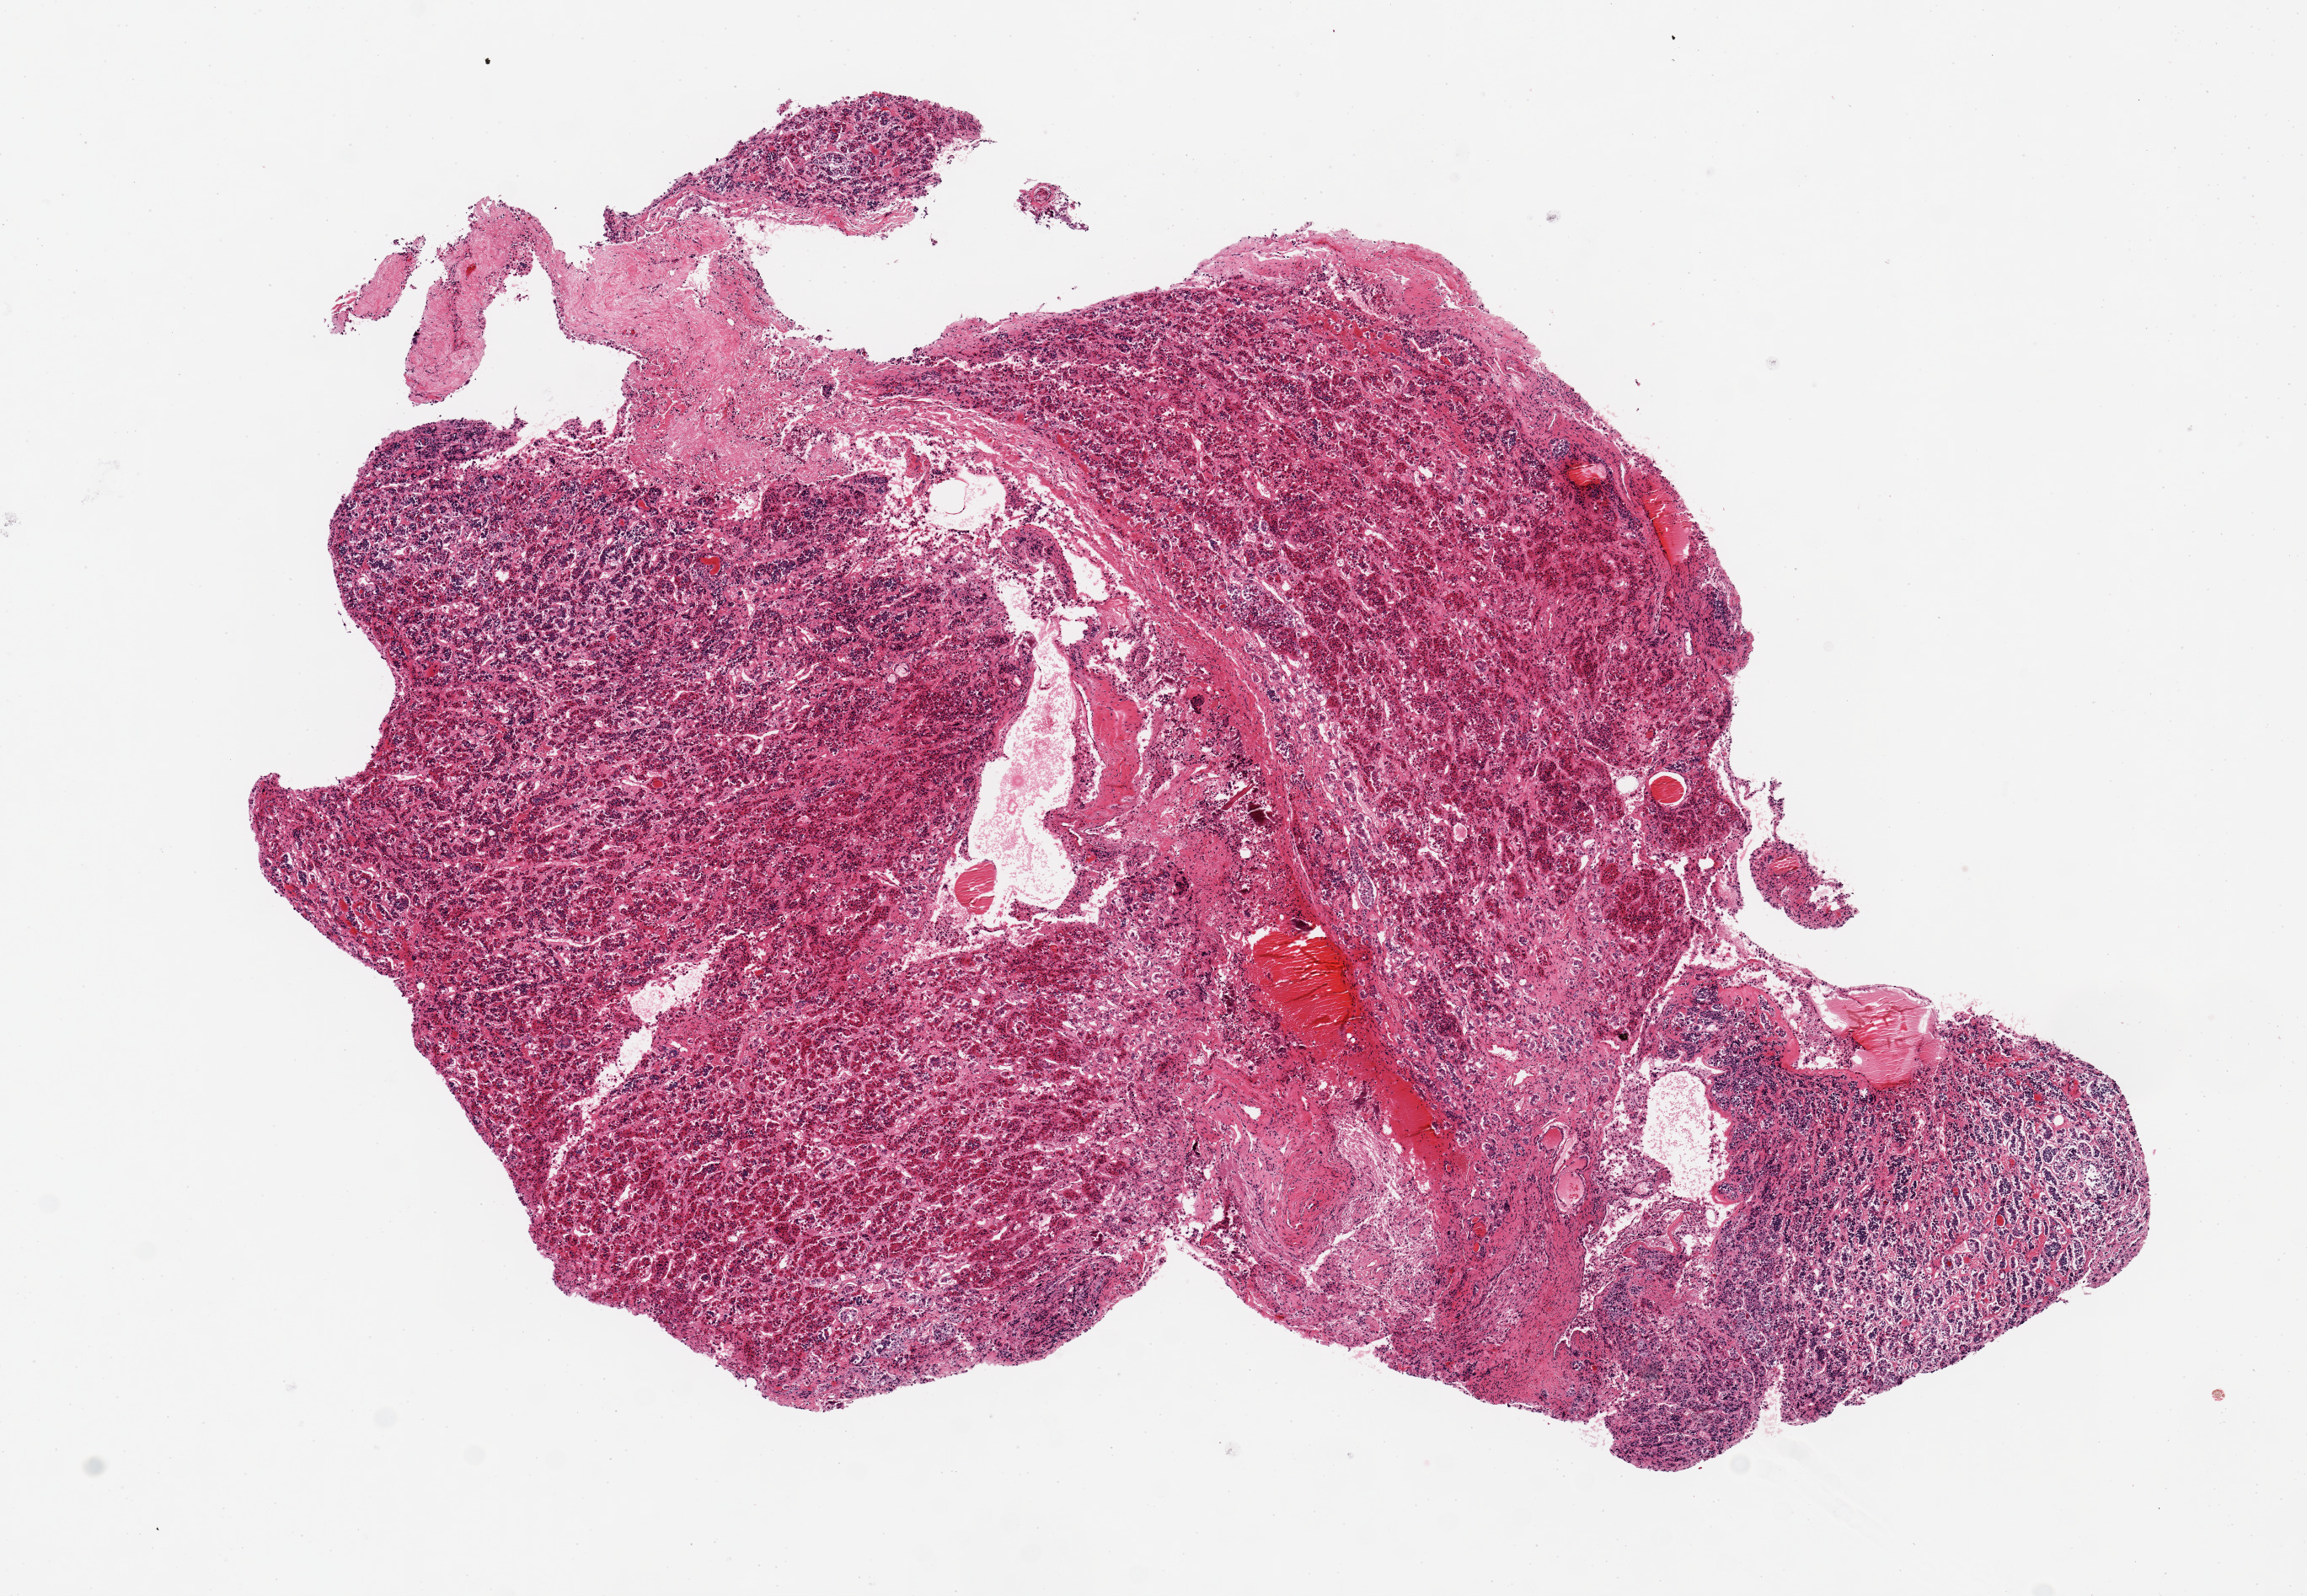
Whole-slide image, H&E stain — whole scanned area (about 10.8 x 7.5 mm, from a 20x scan) shown as a low-resolution overview. PAXgene-fixed paraffin-embedded (PFPE) section. Target tissue: pituitary. Tissue donor sample. Female donor.
- pathologist's review note for this sample: 1 8.5x6mm aliquot